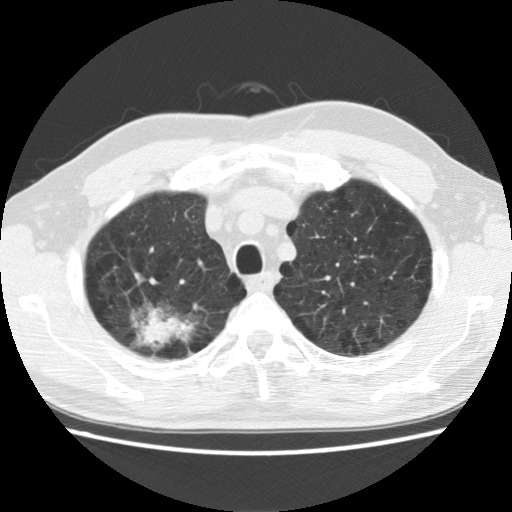
Chest CT (low-dose screening protocol), one axial image; baseline annual screen; lung window (W 1500 / L -600 HU); standard (soft-tissue) reconstruction kernel (STANDARD); 512 × 512 image matrix, field of view 340 × 340 mm. Male, age 64 years at enrolment. Former smoker at enrolment.
Lesion marked by an expert reader, bounding box [x1, y1, x2, y2] px = [112, 292, 201, 364]. Reader record for this screening exam (exam-level; its link to the box is not recorded): non-calcified nodule or mass ≥4 mm, right upper lobe, 39 × 31 mm, spiculated (stellate) margins, mixed attenuation. Official screen result: positive, change unspecified: nodule(s) >= 4 mm or enlarging nodule(s), mass(es), or other non-specific abnormalities suspicious for lung cancer. Later outcome: lung cancer diagnosed 74 days after this screen — adenocarcinoma, NOS, right upper lobe, moderately differentiated (G2), stage IB (AJCC 6th edition), 40 mm at pathology.